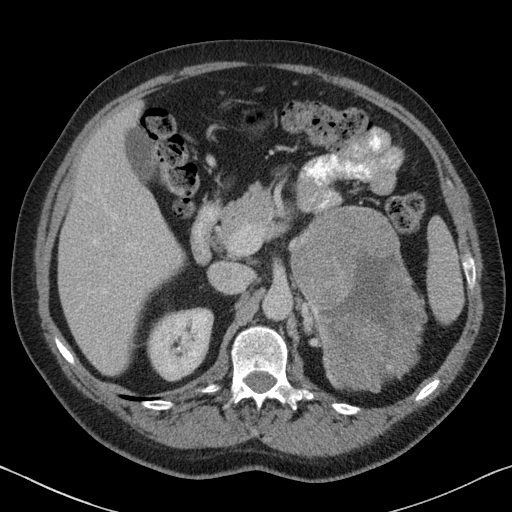
Contrast-enhanced abdominal CT, one axial slice. Position 47 of 88 along the scan axis. Reconstruction kernel B31f. 120 kVp. Soft-tissue window (W 400 / L 40 HU). 3 mm slice thickness. 512 × 512 image matrix, field of view 366 × 366 mm. Patient: male, 51 years. From the clinical record (not read from this slice): diagnosis: adrenocortical carcinoma; tumour side: left adrenal; tumour size at pathology: 16.5 cm; Ki-67 index: 30 %; stage (as recorded): 2.
Outlined on this slice (semi-automatic segmentation, software-assisted and operator-edited):
- mass: box from (x=291, y=206) to (x=426, y=392) px